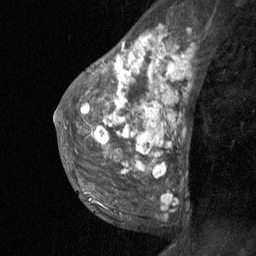
Breast MRI (dynamic contrast-enhanced), one sagittal slice. Position 38 of 64 along the scan axis. Dynamic contrast-enhanced study with each time point stored as its own series, time point 2 of 3 at this slice position (early post-contrast, ordered by acquisition time). 1.5 T. TE 4.8 ms, TR 27 ms. 2 mm slice thickness. 256 × 256 image matrix, field of view 180 × 180 mm. Patient: female, 36 years. From the clinical record (not read from this slice): setting: breast cancer imaged before/during neoadjuvant chemotherapy; receptor status: HR-positive, HER2-negative.
Structures marked on this image (semi-automatically segmented with operator editing):
- analysis volume of interest (the breast-tissue region the enhancement analysis was run in; not a lesion): bounding box [x1, y1, x2, y2] px = [67, 12, 186, 223]
- tumour enhancement mask (voxels above the 90 % enhancement threshold inside the analysis volume of interest): [82, 34, 158, 171]